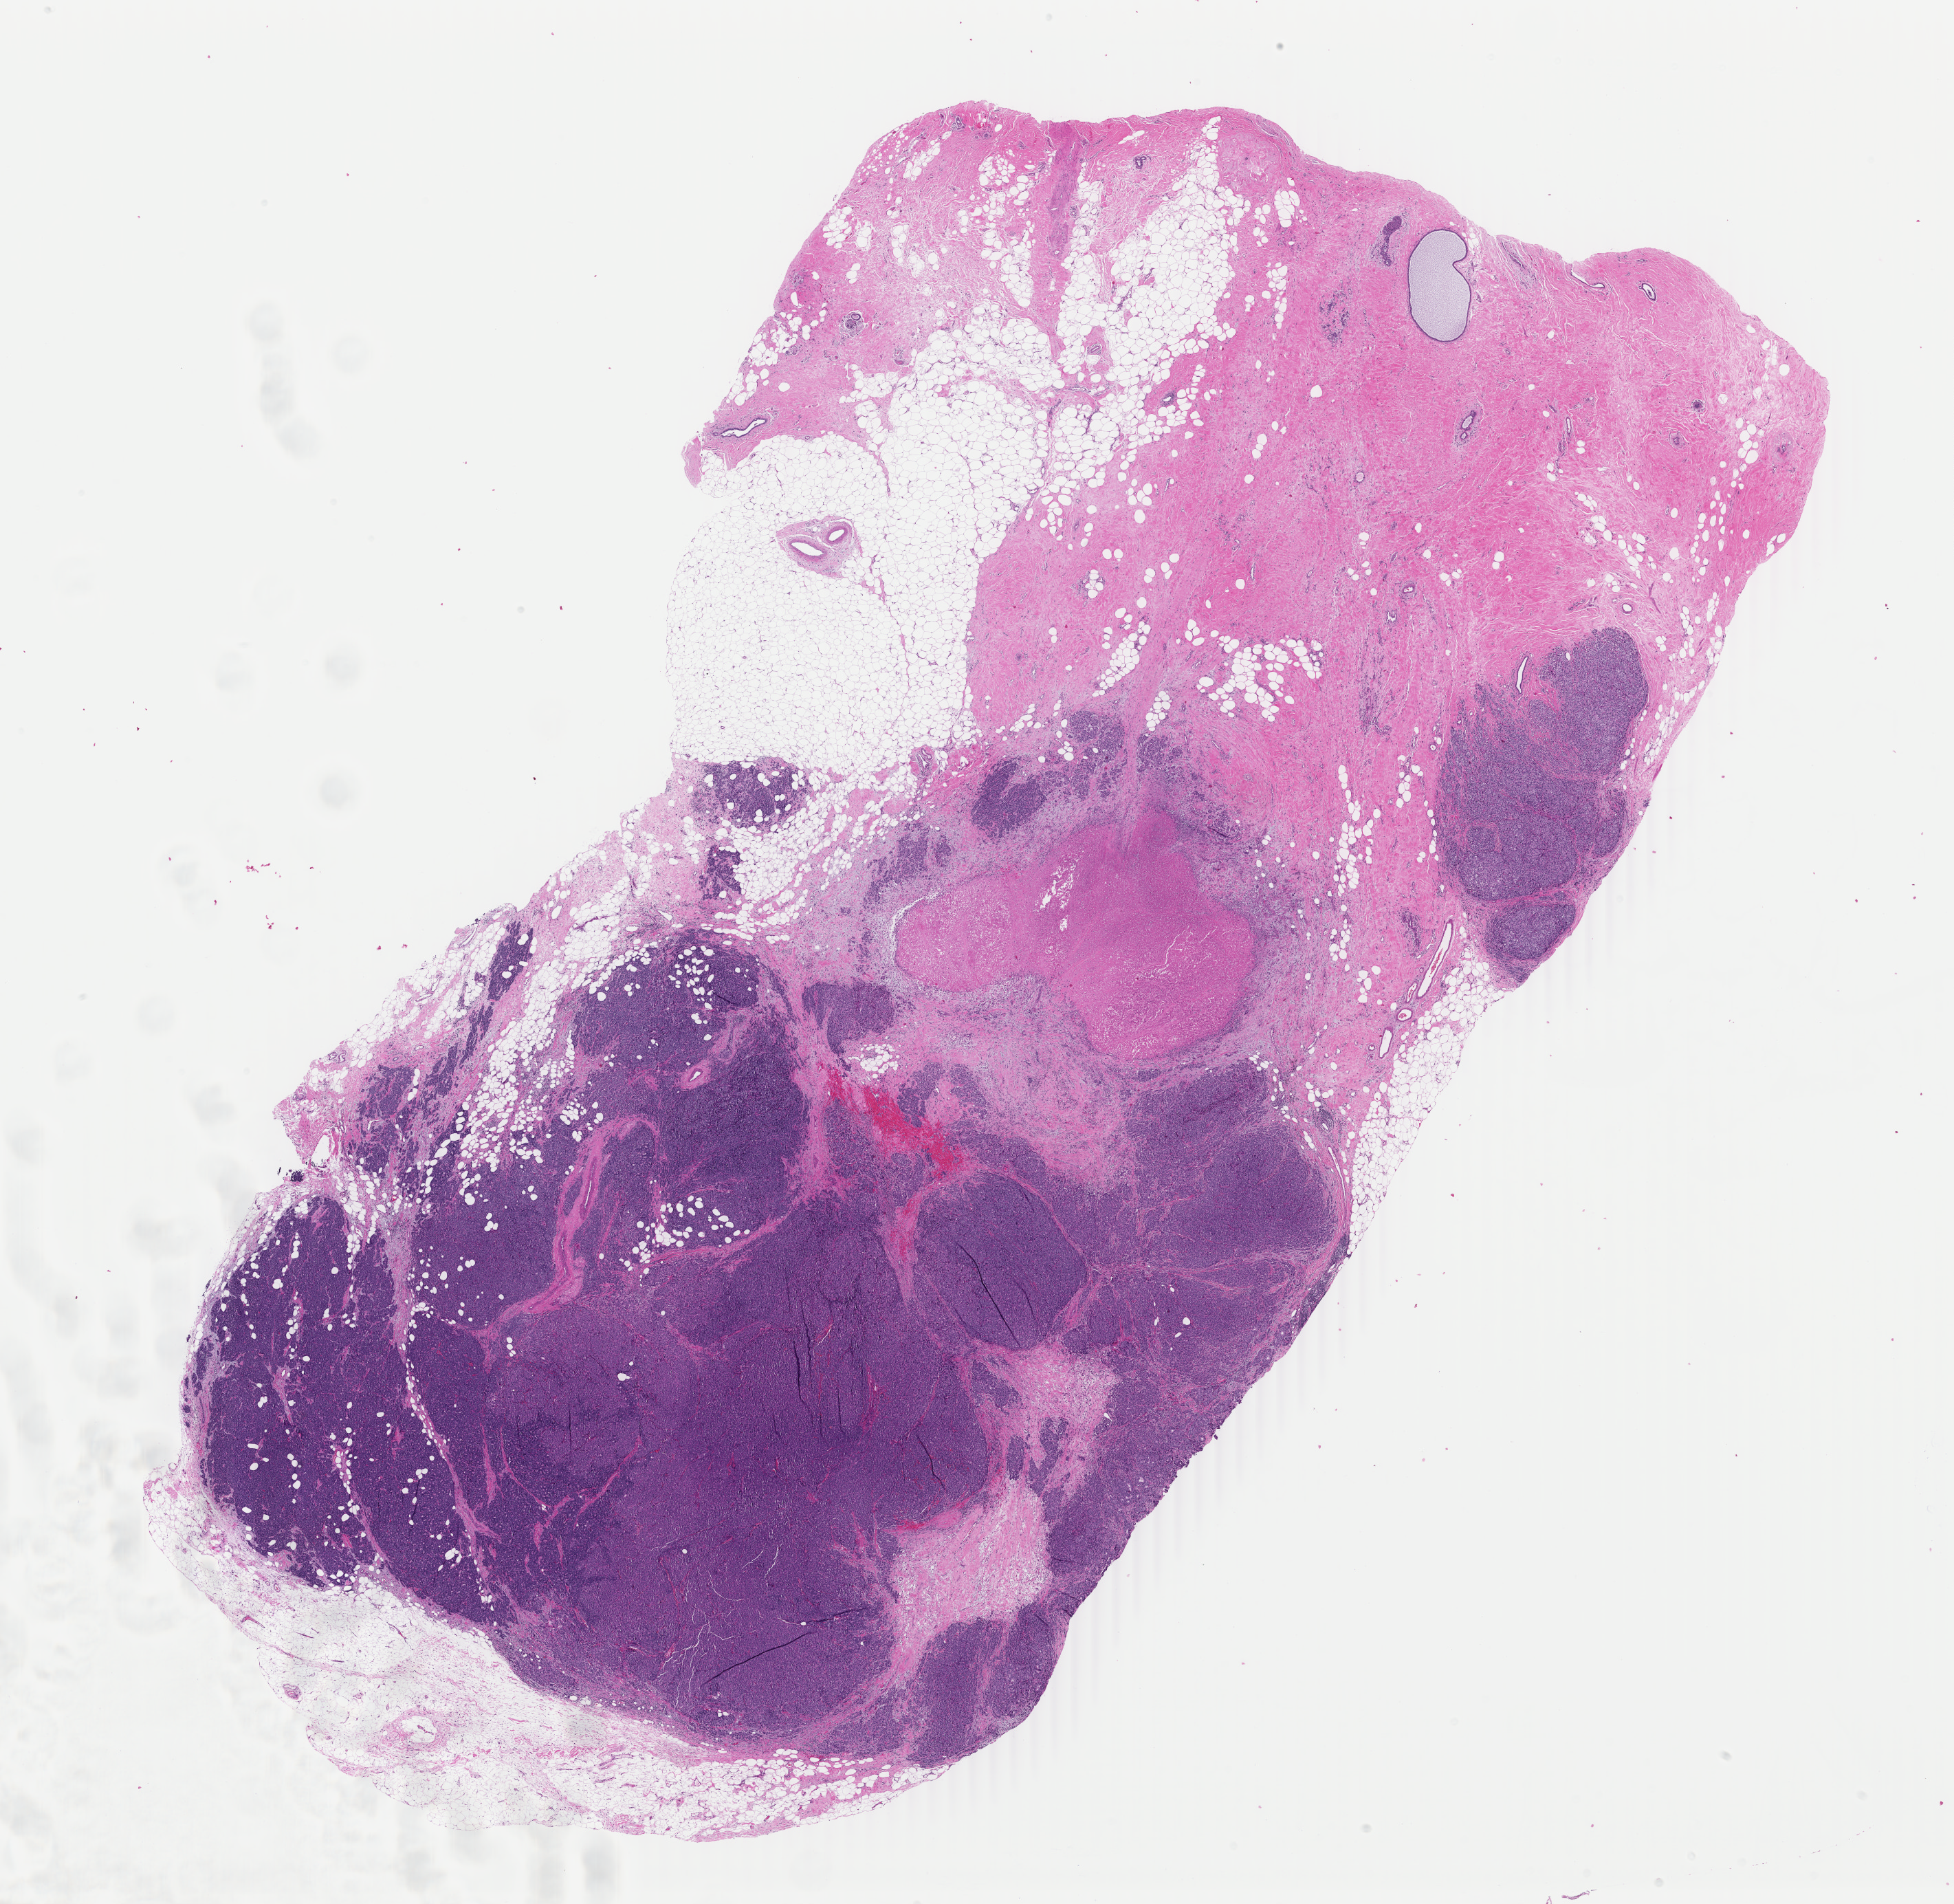
Whole-slide histology image, H&E-stained — low-resolution overview of the scanned area, about 22.6 x 22.0 mm; formalin-fixed paraffin-embedded (FFPE) diagnostic section; primary tumour sample from the breast. Patient: female, age at initial diagnosis 58 years.
• laterality: right
• diagnosis: Infiltrating duct carcinoma, NOS
• lymph nodes positive (case pathology): 5 of 15 examined
• AJCC pathologic stage: IIIA